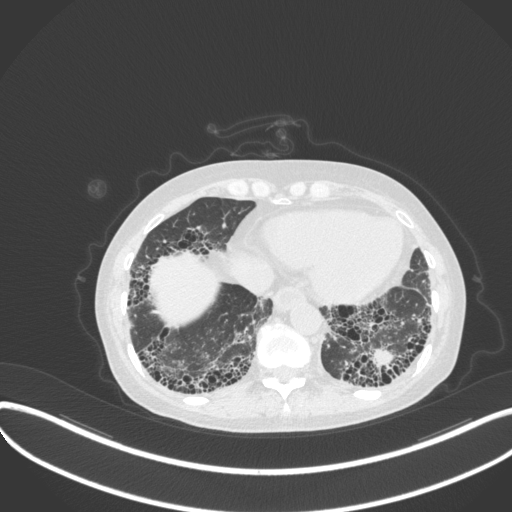
Chest CT, one axial slice. Slice 71 of 373 in the series (ordered by position). Reconstruction kernel B31f. 120 kVp. Lung window (W 1500 / L -600 HU). 1 mm slice thickness. 512 × 512 image matrix, field of view 400 × 400 mm. Patient: female, 56 years. From the clinical record (not read from this slice): clinical TNM (as recorded): T1 N0 M0.
Structures marked on this image (bounding box drawn by a radiologist):
- lung tumour (recorded histology: adenocarcinoma): bounding box (x1, y1, x2, y2) in pixels: (362, 346, 395, 375)